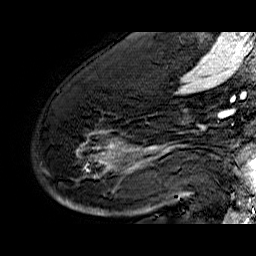
Breast MRI (dynamic contrast-enhanced), one sagittal slice. Slice 40 of 60 in the series (ordered by position). Dynamic contrast-enhanced series, time point 2 of 6 at this slice position (early post-contrast). 1.5 T. TE 6.4 ms, TR 32.9 ms. 256 × 256 image matrix. Female patient. Case-level facts recorded for this patient, not image findings: setting: breast cancer imaged before/during neoadjuvant chemotherapy; receptor status: HR-positive, HER2-negative.
Outlined on this slice (semi-automatic segmentation, software-assisted and operator-edited):
- analysis volume of interest (the breast-tissue region the enhancement analysis was run in; not a lesion): bounding box [x1, y1, x2, y2] px = [53, 74, 176, 210]
- tumour enhancement mask (voxels above the 100 % enhancement threshold inside the analysis volume of interest): [58, 132, 176, 200]